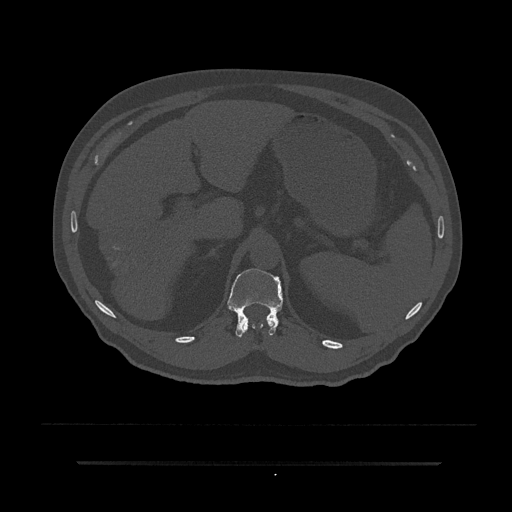
CT including the spine, one axial slice; bone window (W 1800 / L 400 HU); 512 × 512 image matrix. Patient: male, 59 years. From the clinical record (not read from this slice): primary cancer: bile ducts; vertebrae with lytic lesions (as recorded): T10.
Structures marked on this image (semi-automatically segmented with operator editing):
- T11 vertebra: box from (x=244, y=318) to (x=275, y=330) px
- T12 vertebra: (x=228, y=268)–(x=283, y=337)